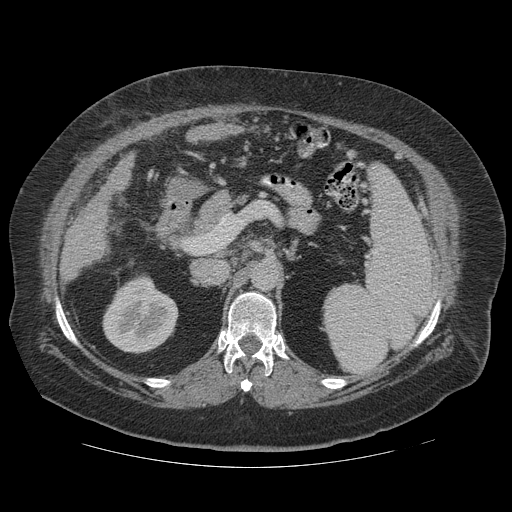
Contrast-enhanced abdominal CT (liver protocol), one axial slice. Slice 59 of 121 in the series (ordered by position). Reconstruction kernel STANDARD. 140 kVp. Soft-tissue window (W 400 / L 40 HU). 2.5 mm slice thickness. 512 × 512 image matrix. From the clinical record (not read from this slice): diagnosis: hepatocellular carcinoma (patient treated with transarterial chemoembolisation; whether this scan precedes or follows treatment is not stated here); TNM stage (as recorded): Stage-IIIA; Child-Pugh class: A; tumour size: 7.4 cm.
Annotated regions visible in this slice (semi-automatic segmentation, software-assisted and operator-edited):
- liver parenchyma outside the tumour (the mass and vessels are separate outlines, so this box may not span the whole liver): box from (x=60, y=156) to (x=132, y=280) px